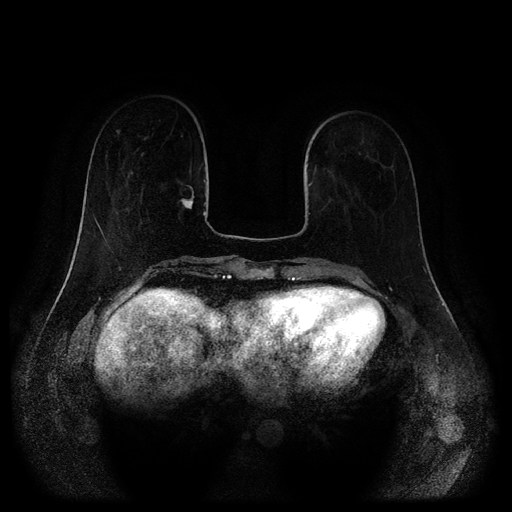
Breast MRI (dynamic contrast-enhanced, multi-phase), one axial slice; slice 35 of 116 in the series (ordered by position); dynamic contrast-enhanced series, time point 2 of 5 at this slice position (early post-contrast); 1.5 T; TE 2.6 ms, TR 5.2 ms; 2 mm slice thickness; 512 × 512 image matrix, field of view 380 × 380 mm. Patient: female, 62 years.
Structures marked on this image (semi-automatic segmentation, software-assisted and operator-edited):
- breast lesion (labelled 'tumour' in the annotation; benign lesions carry a separate 'benign' label): bounding box [x1, y1, x2, y2] px = [178, 184, 195, 210]